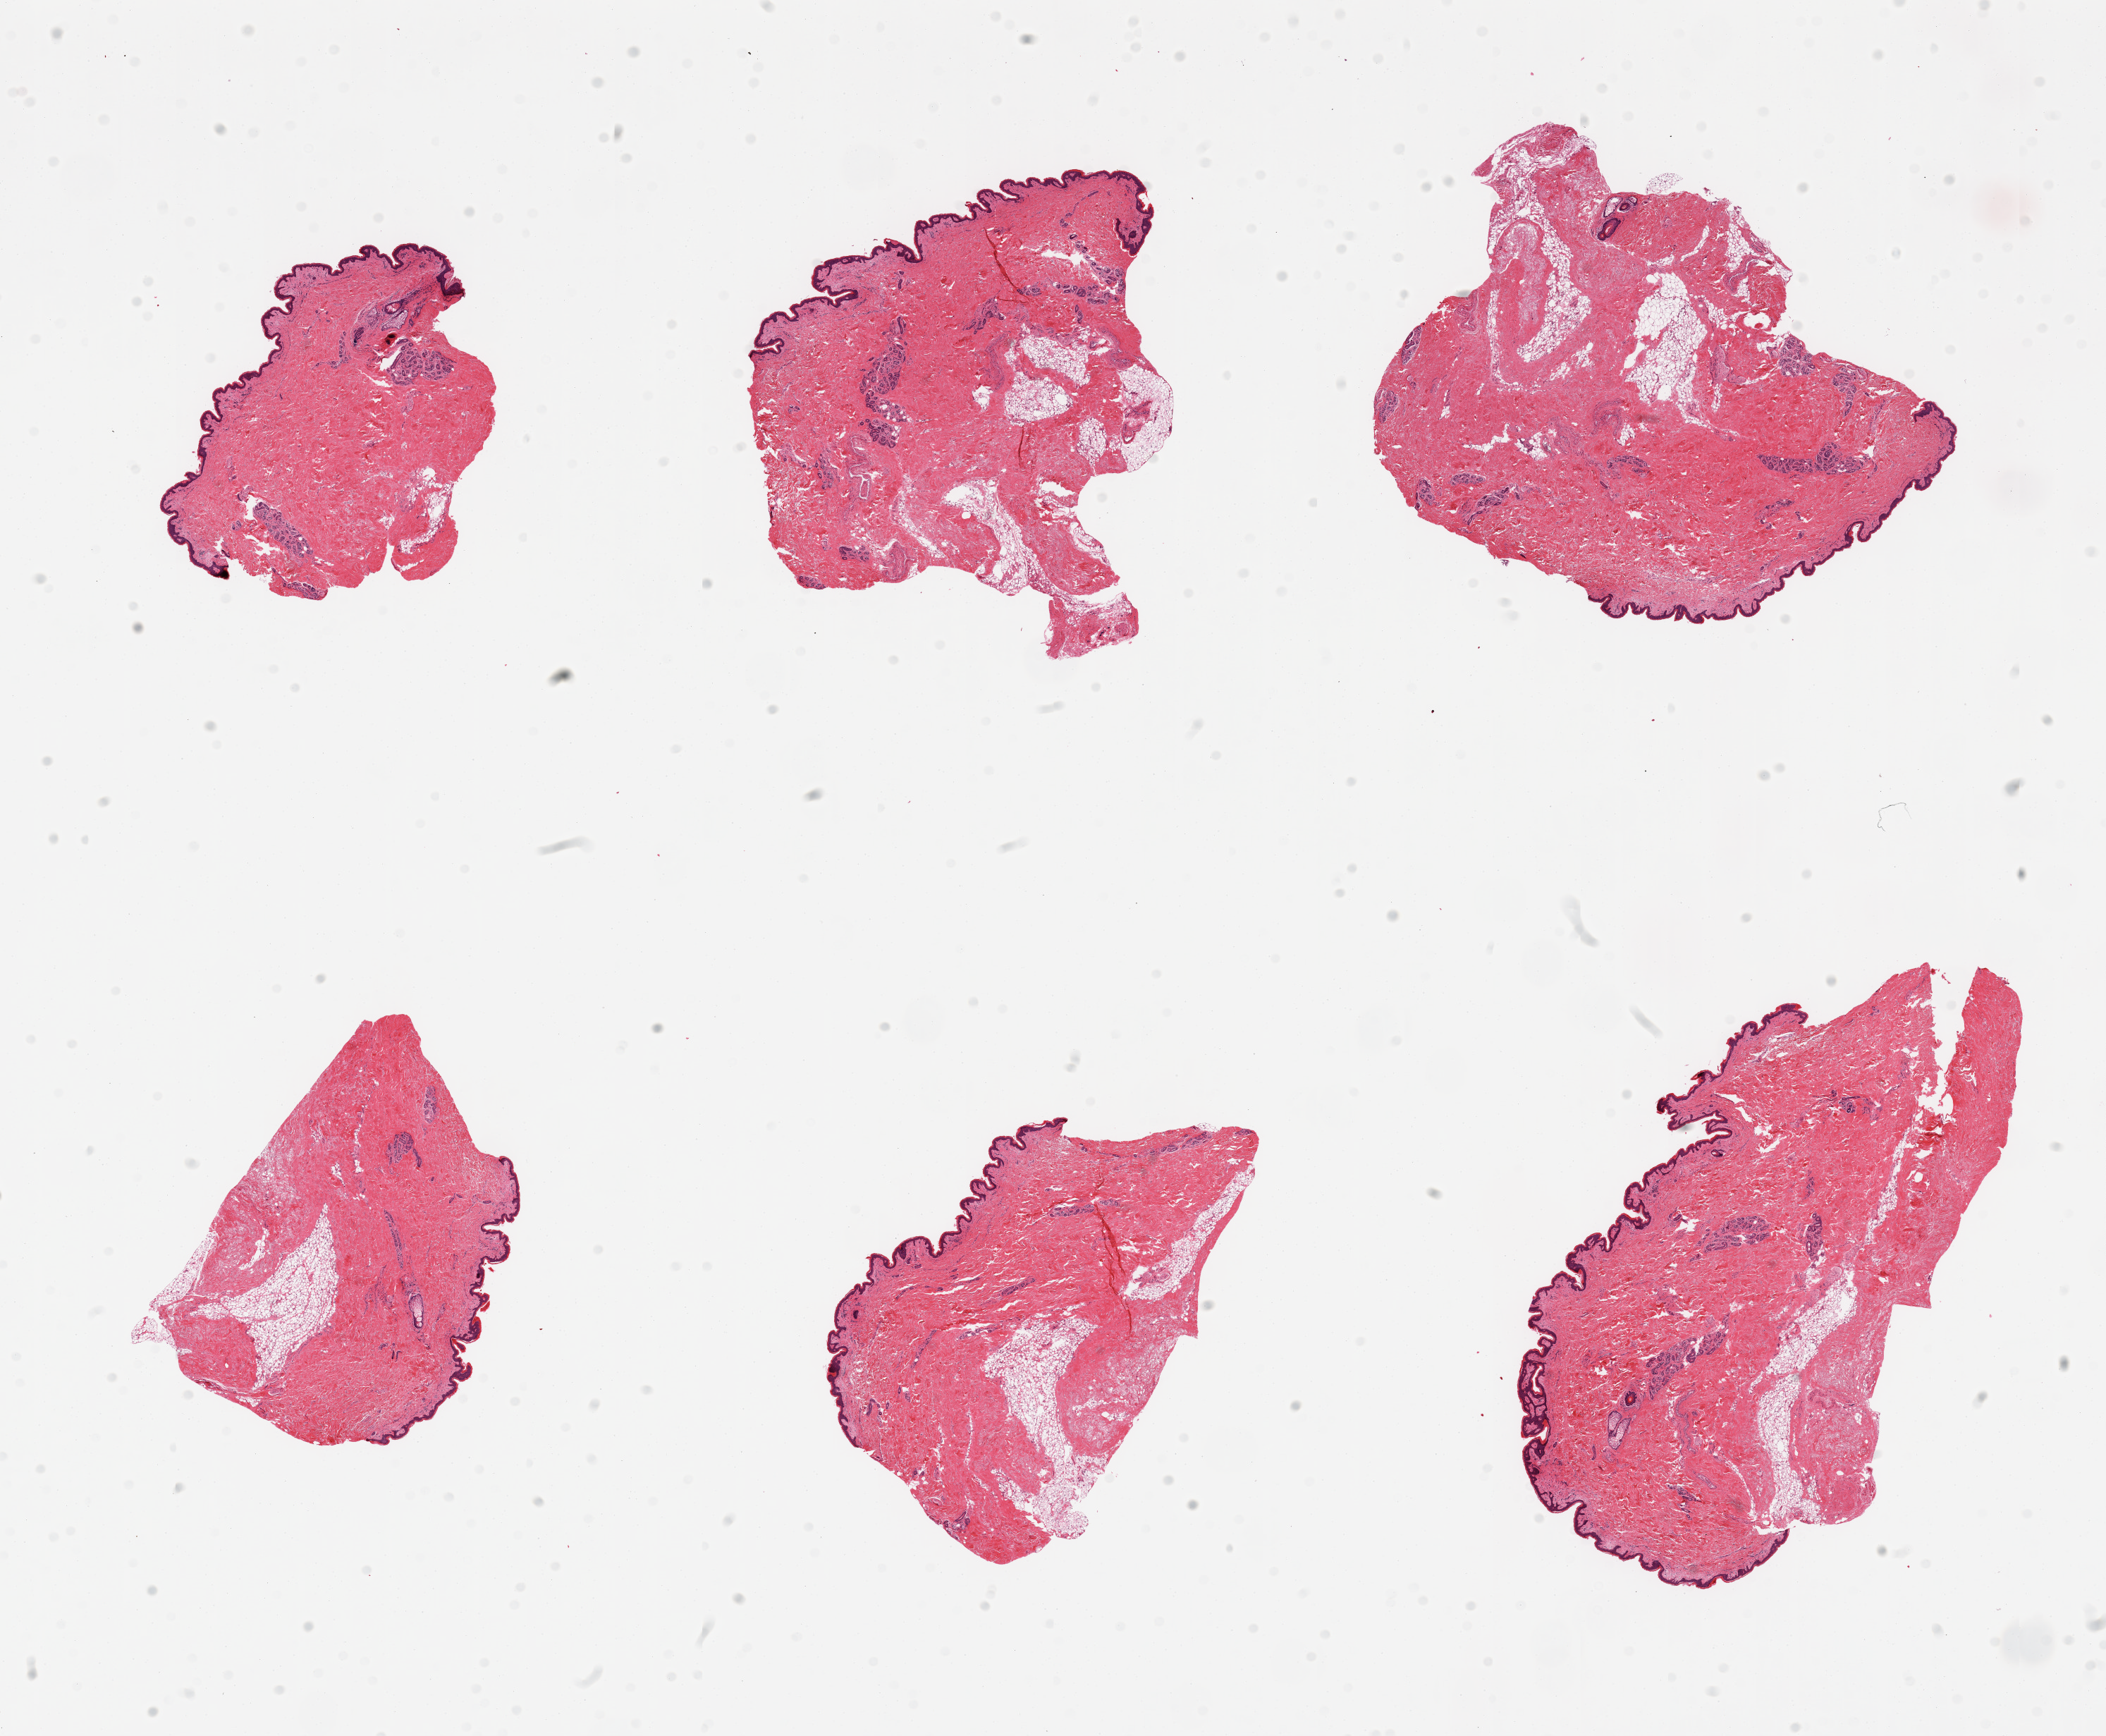
Digitized hematoxylin and eosin (H&E)-stained section — a low-resolution overview of the entire scanned area, about 23.6 x 19.5 mm (acquisition: 20x scan); PAXgene-fixed, paraffin-embedded tissue; target tissue: skin of suprapubic region; tissue donor sample.
Review note (as recorded): 6 pieces, well trimmed, but some pieces include up to 10% internal fat.